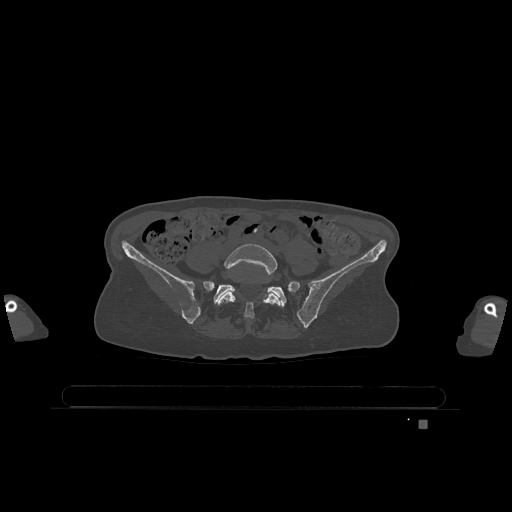
CT including the spine, one axial slice. Slice 220 of 1317 in the series (ordered by position). Bone window (W 1800 / L 400 HU). 0.5 mm slice thickness. 512 × 512 image matrix, field of view 500 × 500 mm. Patient: female, 74 years. From the clinical record (not read from this slice): primary cancer: lung.
Outlined on this slice (semi-automatic segmentation, software-assisted and operator-edited):
- L5 vertebra: bounding box (x1, y1, x2, y2) in pixels: (216, 244, 281, 319)